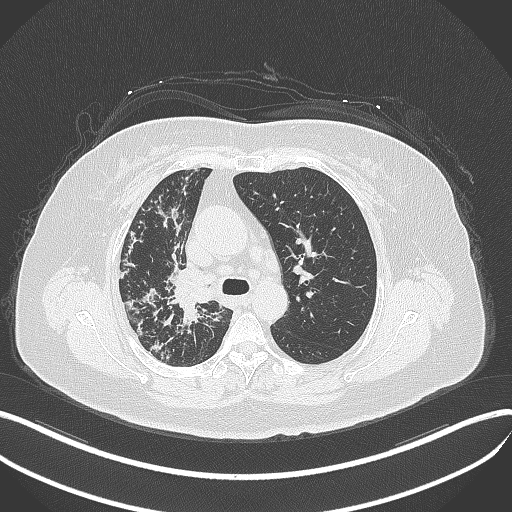
Chest CT, one axial slice. Position 243 of 376 along the scan axis. Reconstruction kernel B70f. Lung window (W 1500 / L -600 HU). 1 mm slice thickness. 512 × 512 image matrix, field of view 400 × 400 mm. Female patient, age 60 years. Case-level facts recorded for this patient, not image findings: clinical TNM (as recorded): T1c N0 M0; histopathological grade: G1-G2.
Outlined on this slice (rectangle marked by the reading radiologist):
- lung tumour (recorded histology: squamous cell carcinoma): bounding box (x1, y1, x2, y2) in pixels: (170, 271, 212, 310)